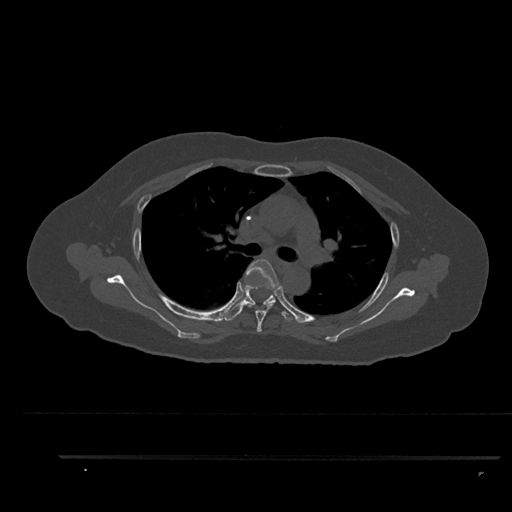
CT including the spine, one axial slice; position 622 of 797 along the scan axis; bone window (W 1800 / L 400 HU); 512 × 512 image matrix. Female patient, age 44 years. Case-level facts recorded for this patient, not image findings: primary cancer: renal.
Annotated regions visible in this slice (semi-automatically segmented with operator editing):
- T4 vertebra: box from (x=243, y=259) to (x=281, y=332) px
- T5 vertebra: (x=225, y=285)–(x=293, y=321)